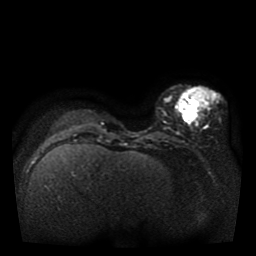
Breast MRI, one axial slice. Position 13 of 41 along the scan axis. Diffusion-weighted series; image 2 of 4 stored at this slice position (different b-values; order by instance number). 1.5 T. 256 × 256 image matrix, field of view 330 × 330 mm. Female patient.
Outlined on this slice (expert manual segmentation):
- tumour on diffusion-weighted imaging: bounding box <183,108,196,117> (left, top, right, bottom; pixels)